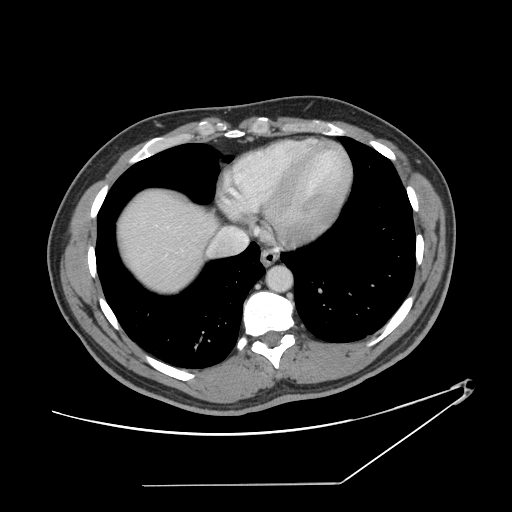
Contrast-enhanced abdominal CT, one axial slice. Slice 135 of 152 in the series (ordered by position). Reconstruction kernel STANDARD. 120 kVp. Intravenous contrast given. Soft-tissue window (W 400 / L 40 HU). 512 × 512 image matrix. Male patient, age 45 years. Case-level facts recorded for this patient, not image findings: diagnosis: colorectal cancer liver metastases, imaged before liver resection; multiple liver metastases: no; largest metastasis: 1 cm; disease in both lobes: no.
Structures marked on this image (outlined manually by an expert reader):
- hepatic veins: bounding box [x1, y1, x2, y2] px = [156, 226, 248, 245]
- liver: [118, 191, 215, 293]
- planned liver remnant (the part of the liver to remain after resection): [119, 191, 215, 293]